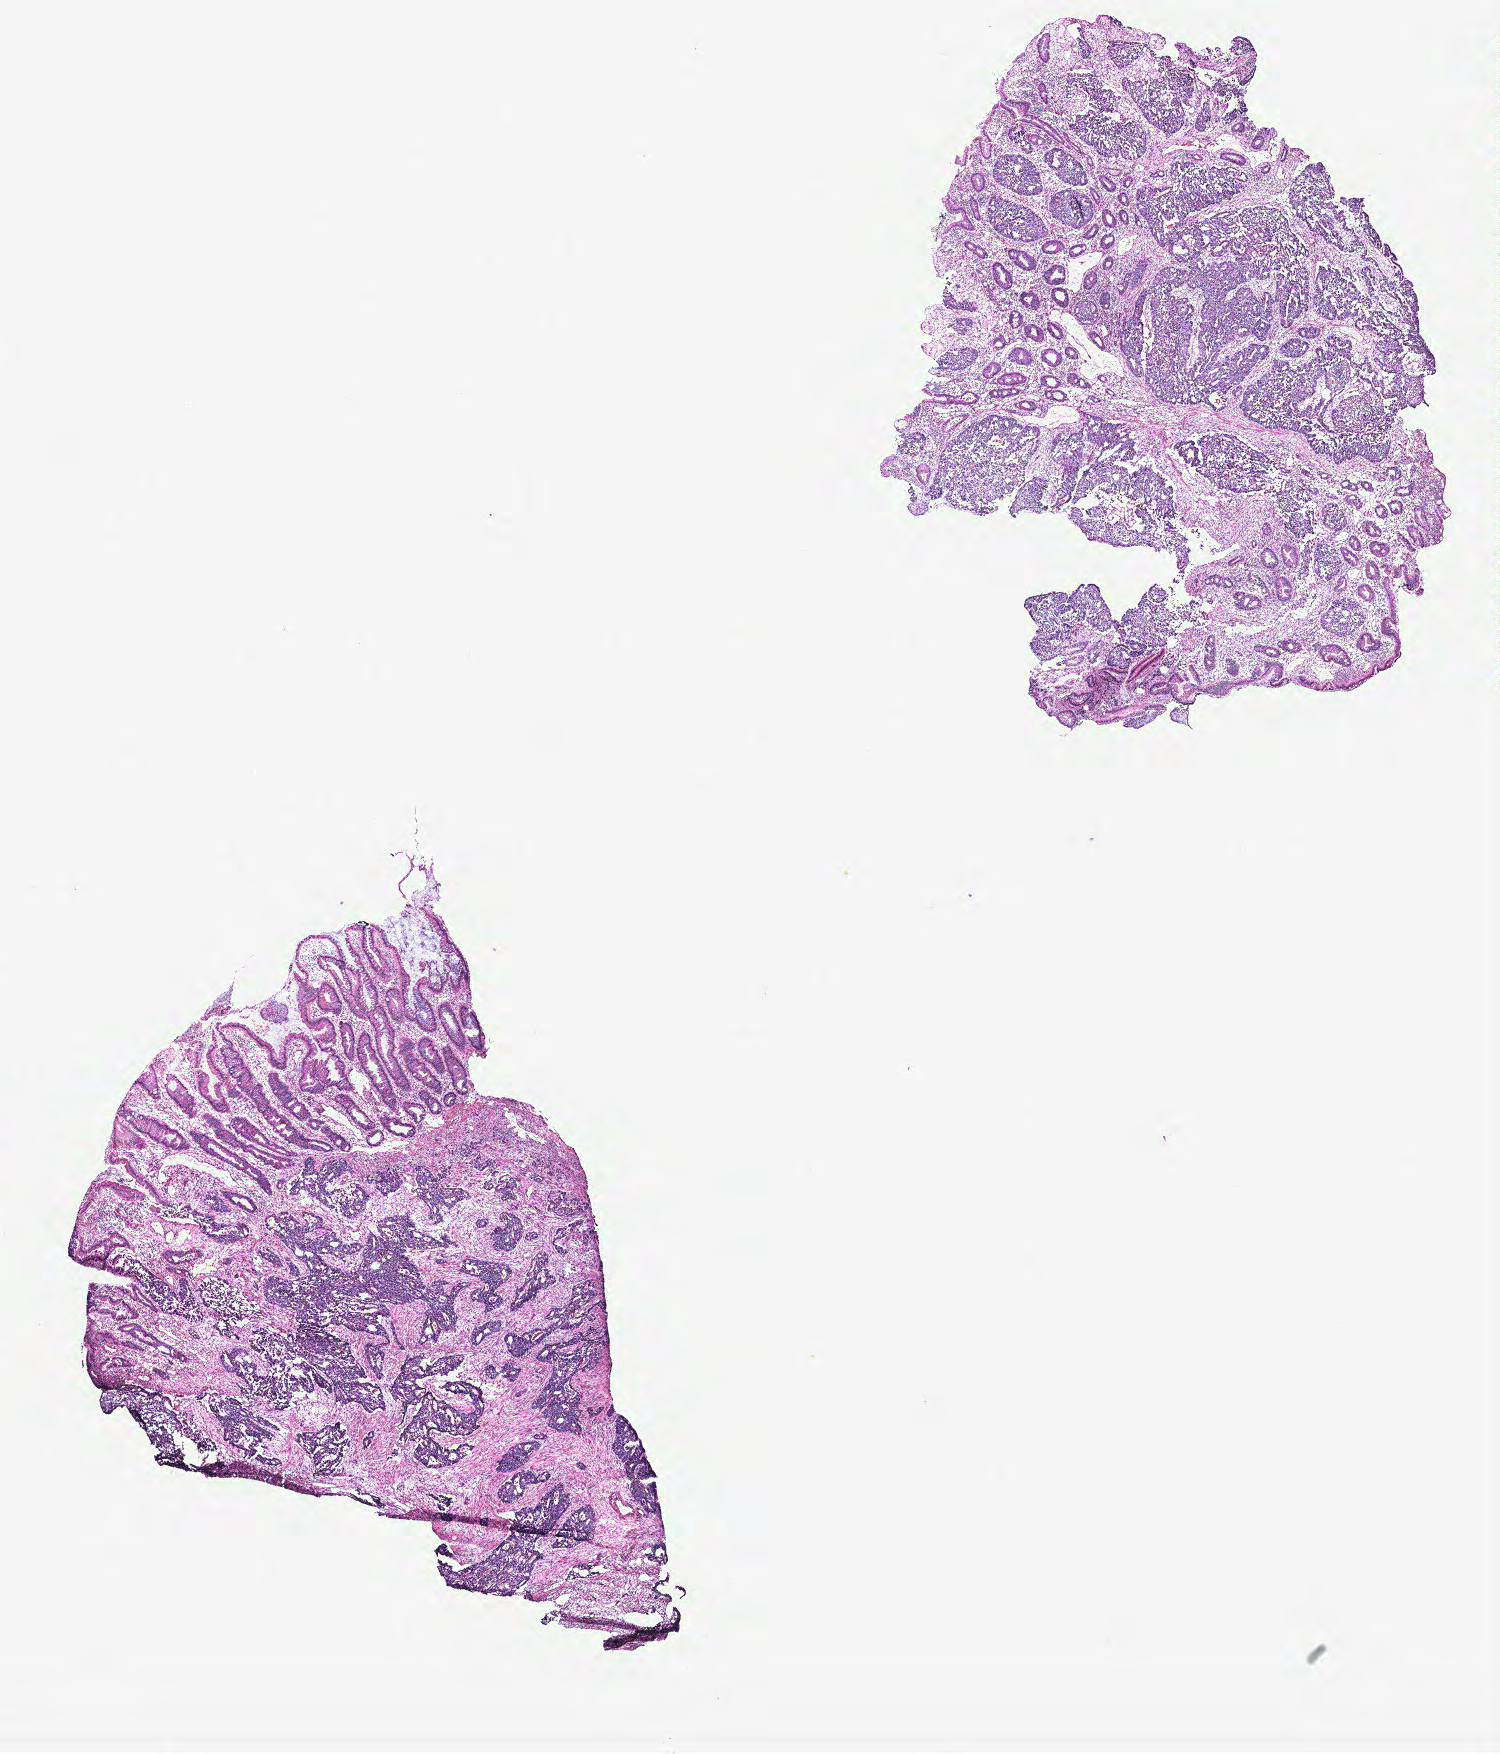
Digitized H&E-stained tissue section (whole slide), shown as a low-resolution overview of the whole scanned area (about 12.0 x 14.0 mm); colon, tissue type not recorded.
Patient diagnosis (cohort enrolment): colon cancer (colon).